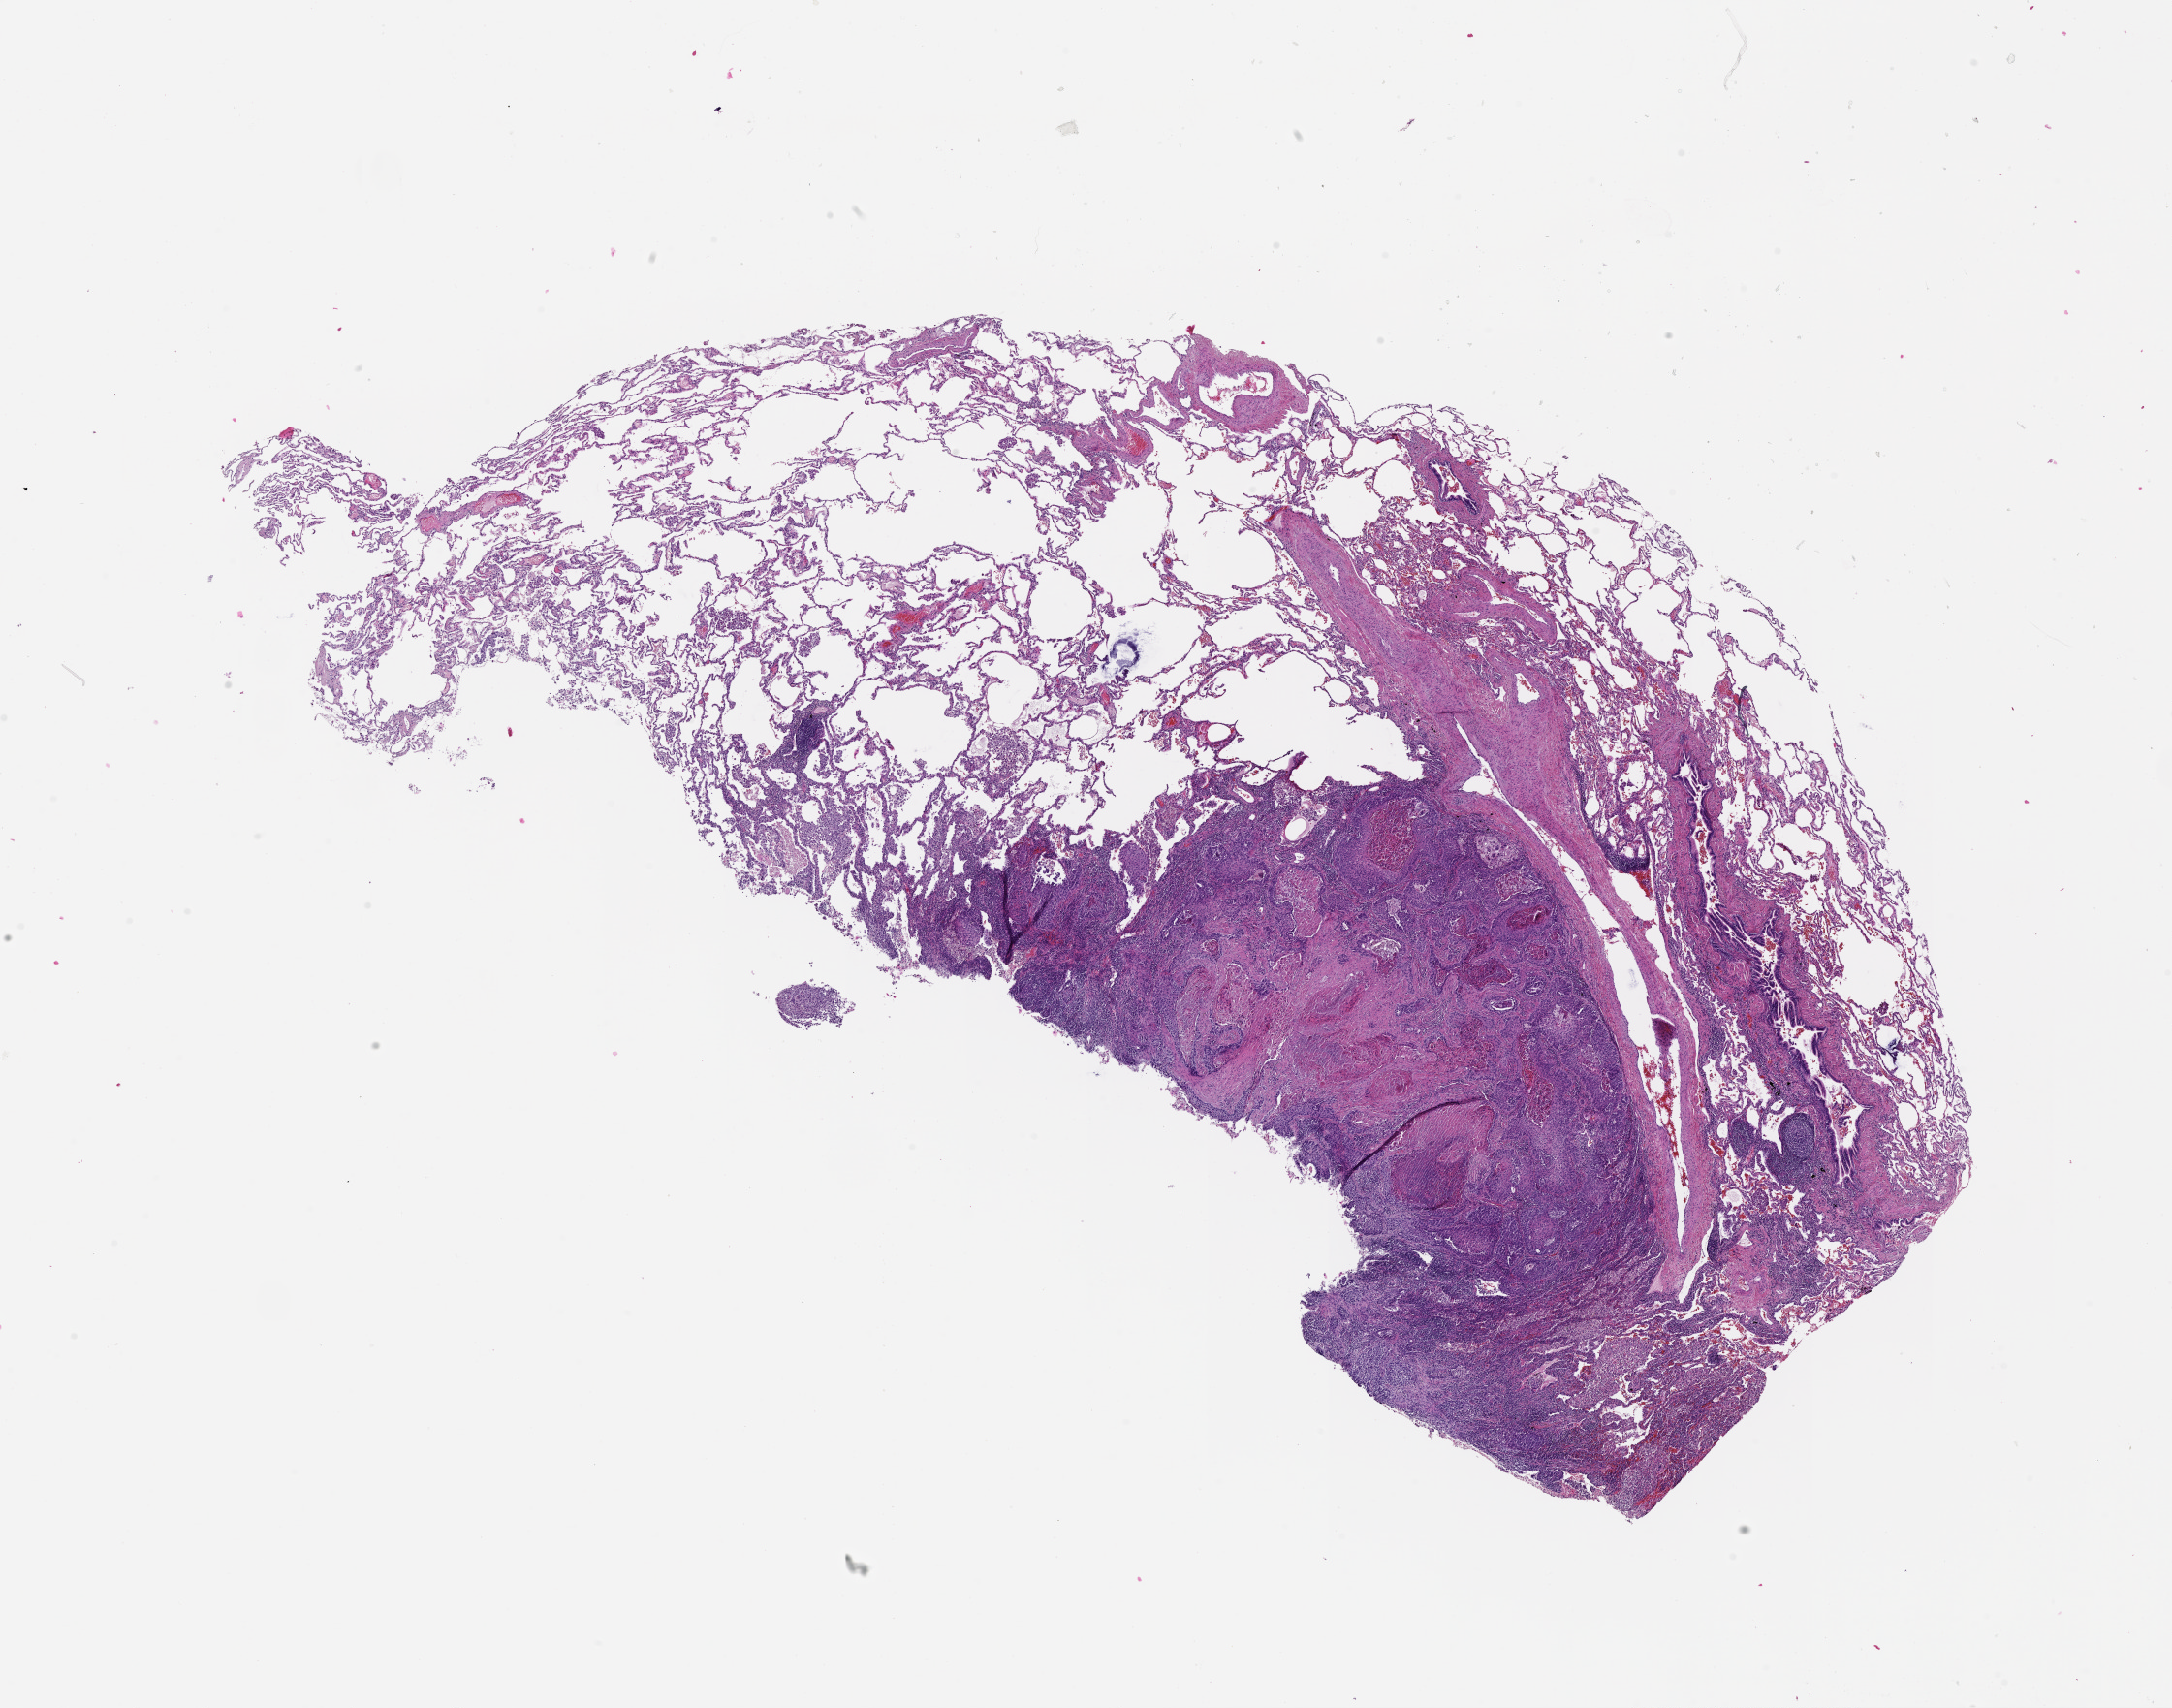
Whole-slide histology image, H&E-stained — shown as a low-resolution overview of the whole scanned area (about 18.0 x 14.2 mm, from a 20x scan), lung, tumour tissue. Male, 67 y/o.
Patient diagnosis (cohort enrolment): squamous cell carcinoma (lung).